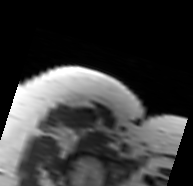
MRI of an extremity soft-tissue mass, one axial slice. Slice 69 of 91 in the series (ordered by position). MR volume resampled by the dataset authors to the PET/CT grid (not the native acquisition matrix). 3.27 mm slice thickness. 193 × 186 image matrix, field of view 188 × 182 mm. Female patient. Case-level facts recorded for this patient, not image findings: histological type: malignant solitary fibrous tumor; grade: intermediate; site of the primary tumour: right thigh.
Annotated regions visible in this slice (expert contour drawn on MRI and transferred to this co-registered scan by the dataset authors):
- gross tumour volume including surrounding oedema: box from (x=58, y=124) to (x=105, y=150) px